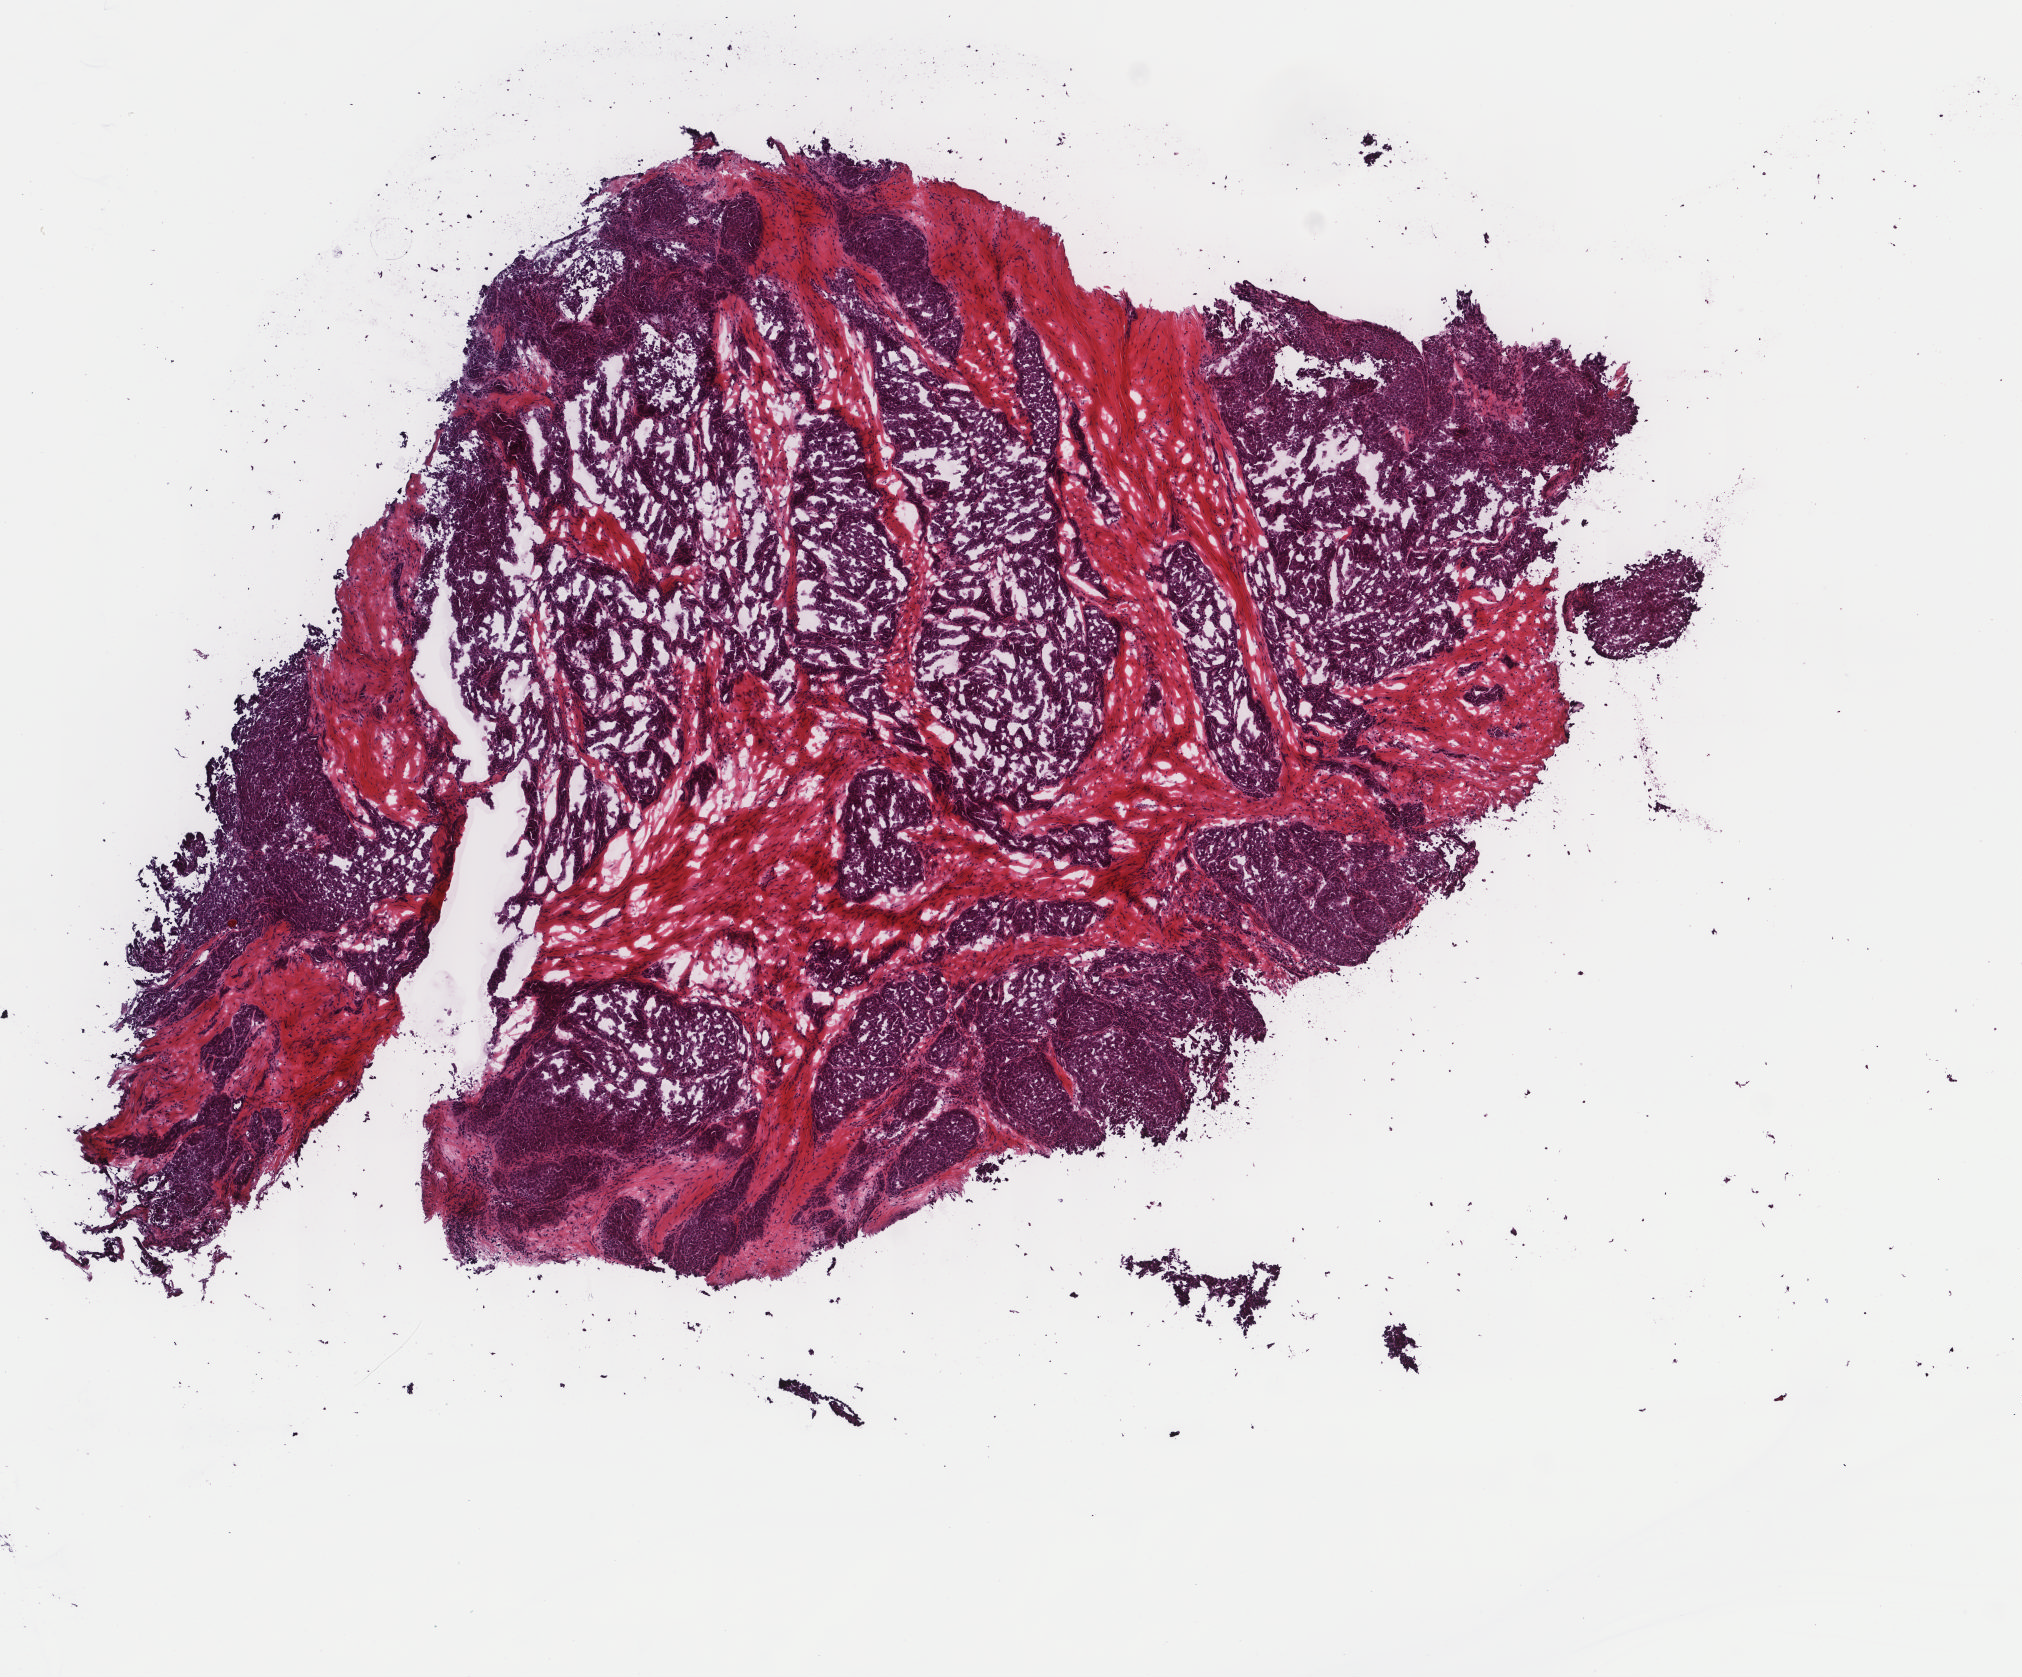
Digitized H&E-stained tissue section (whole slide), a low-resolution overview of the entire scanned area, about 8.0 x 6.7 mm (from a 40x scan). Frozen section from the top of the tissue portion. Thyroid, primary tumour sample. Patient: female, age at initial diagnosis 19 years. Slide review estimates, as recorded: tumour cells 85%, tumour nuclei 85%, normal cells 0%, stromal cells 15%, necrosis 0%. Infiltration values recorded for this section: lymphocyte infiltration 2%, monocyte infiltration 0%, neutrophil infiltration 0%.
• AJCC pathologic stage: I (6th edition)
• laterality: midline
• diagnosis: Papillary adenocarcinoma, NOS (thyroid gland)